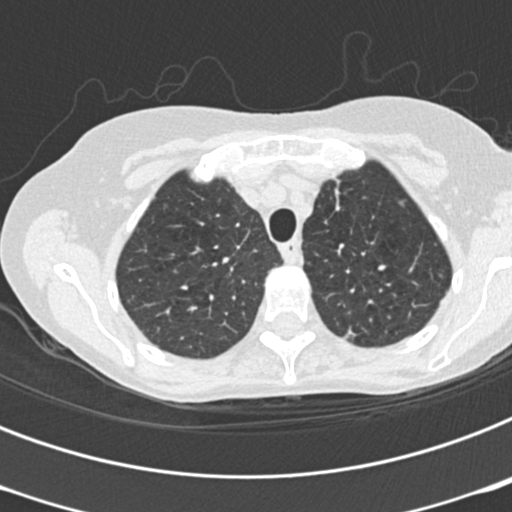
Low-dose screening chest CT, one axial slice; reconstruction kernel B30f; 120 kVp; lung window (W 1500 / L -600 HU); 512 × 512 image matrix, field of view 290 × 290 mm.
Structures marked on this image (expert manual segmentation):
- lesion 2 (nodule, upper lobe of left lung): bounding box <344,326,359,339> (left, top, right, bottom; pixels)